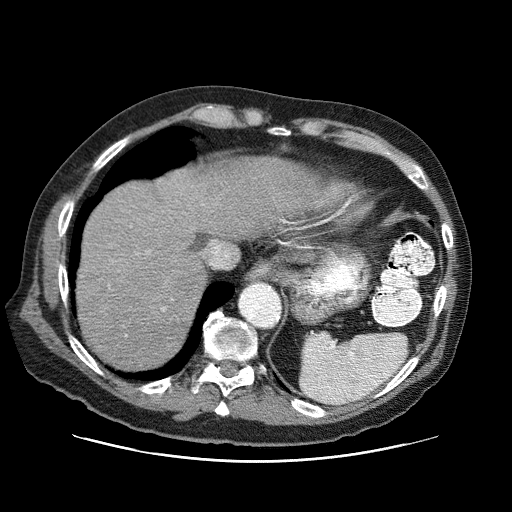
Contrast-enhanced abdominal CT (liver protocol), one axial slice. Position 63 of 87 along the scan axis. Reconstruction kernel STANDARD. One of 3 acquisitions stored at this slice position. Soft-tissue window (W 400 / L 40 HU). 512 × 512 image matrix. Case-level facts recorded for this patient, not image findings: diagnosis: hepatocellular carcinoma (patient treated with transarterial chemoembolisation; whether this scan precedes or follows treatment is not stated here); TNM stage (as recorded): Stage-IIIA; Child-Pugh class: A; tumour differentiation: well differentiated; tumour nodularity: multinodular.
Structures marked on this image (semi-automatic segmentation, software-assisted and operator-edited):
- liver parenchyma outside the tumour (the mass and vessels are separate outlines, so this box may not span the whole liver): bounding box <76,156,330,370> (left, top, right, bottom; pixels)
- liver vessels: <283,220,287,223>